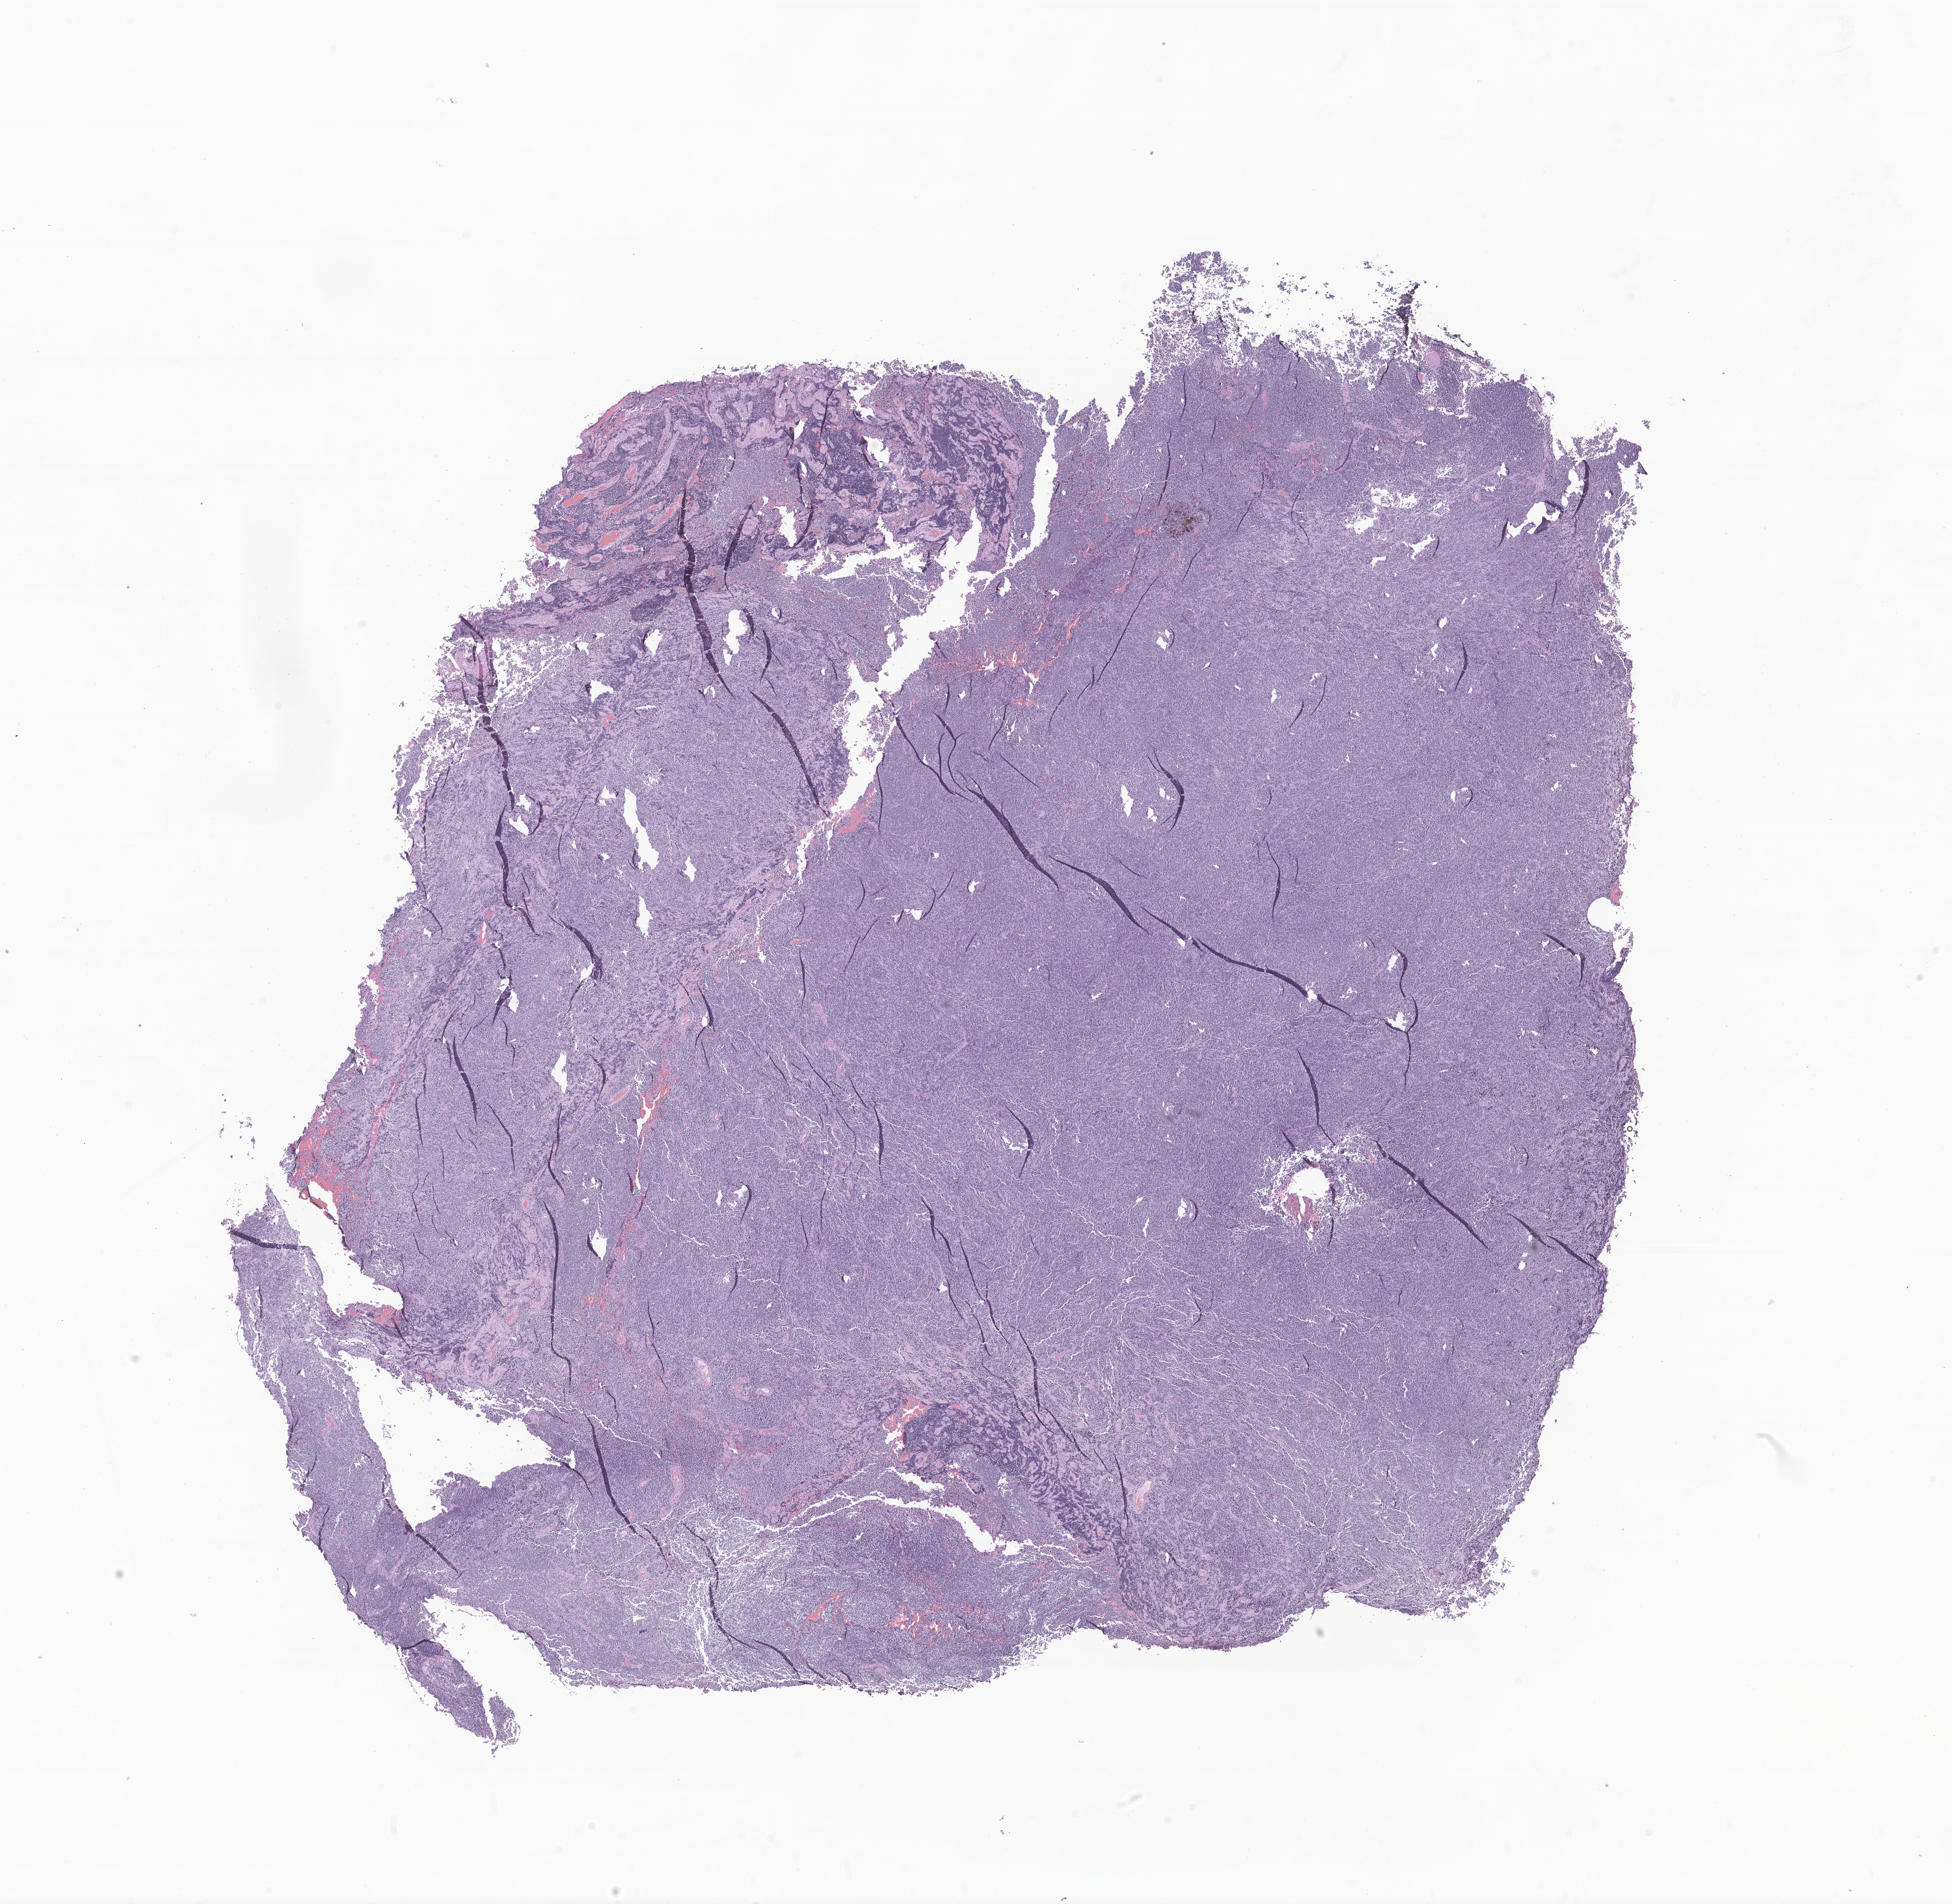
Whole-slide image, haematoxylin and eosin stain of tumor tissue from the cerebellum — whole scanned area (about 17.6 x 17.2 mm) shown as a low-resolution overview; FFPE section. Patient male; age 183 months (15 years 3 months).
* recorded diagnosis: Medulloblastoma, NOS